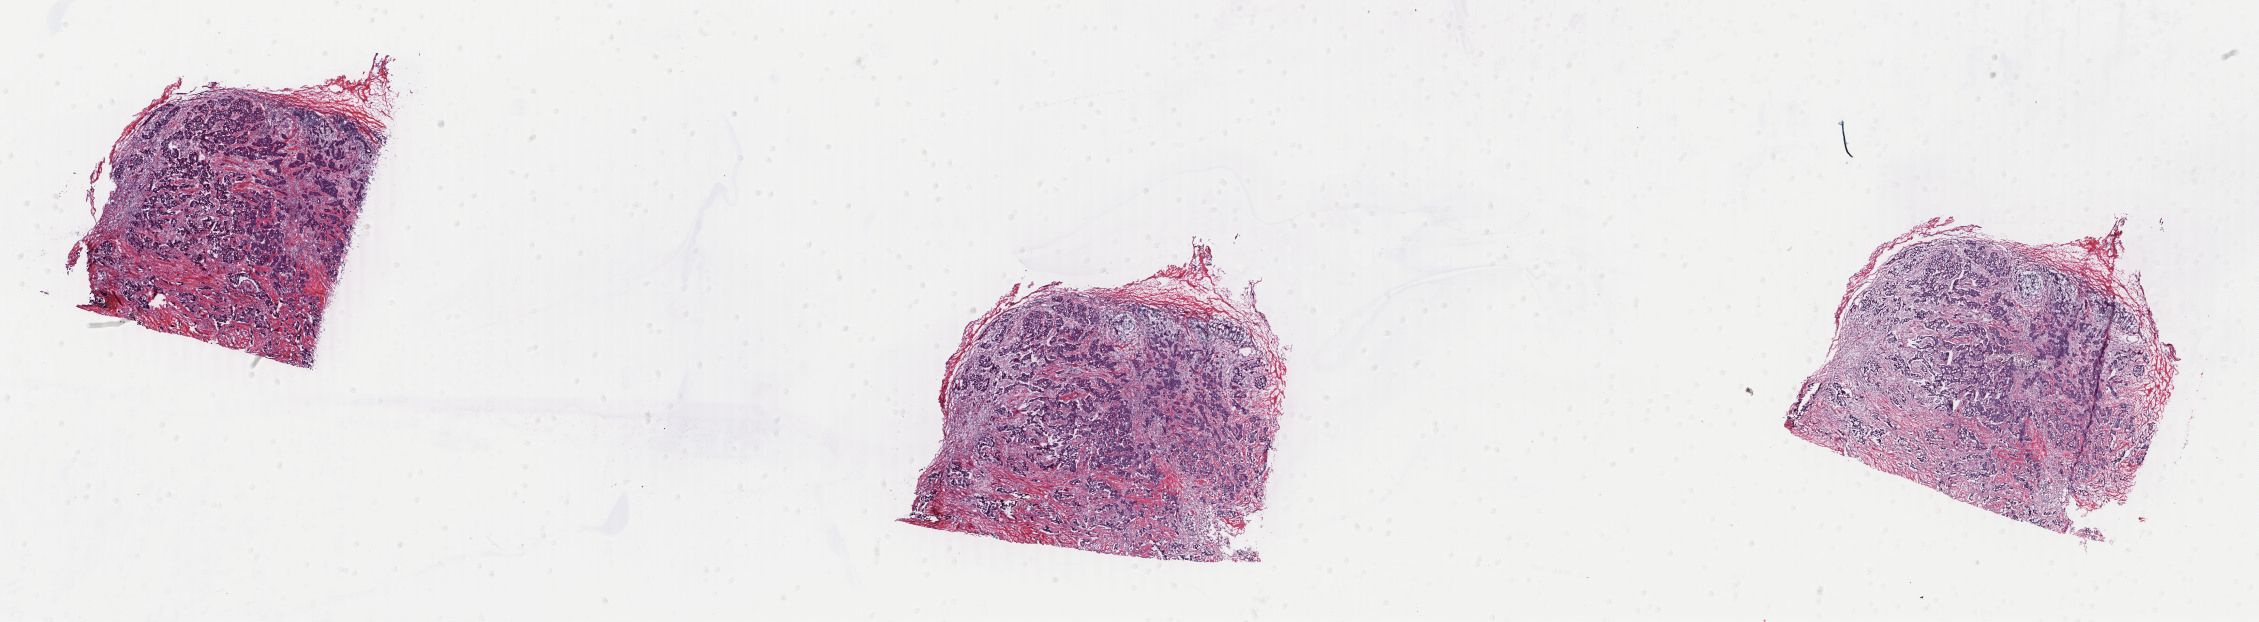
Digitized H&E-stained tissue section (whole slide), a low-resolution overview of the entire scanned area, about 35.9 x 9.9 mm, frozen section, breast, primary tumour sample. Female, age 42 years at initial diagnosis.
Diagnosis: Infiltrating duct carcinoma, NOS.